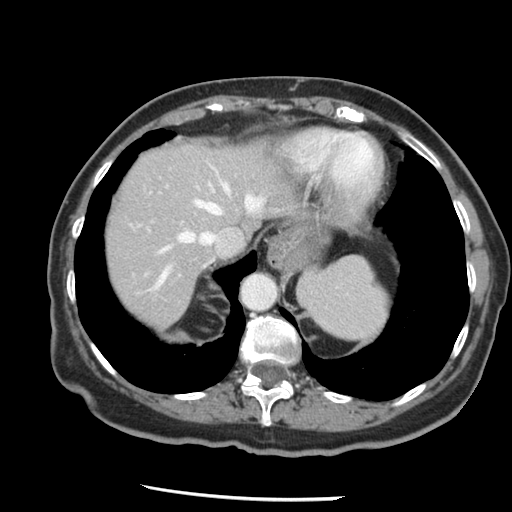
Contrast-enhanced abdominal CT, one axial slice. Position 111 of 148 along the scan axis. Reconstruction kernel STANDARD. 120 kVp. Intravenous contrast given. Soft-tissue window (W 400 / L 40 HU). 2.5 mm slice thickness. 512 × 512 image matrix. Female patient, age 85 years. Case-level facts recorded for this patient, not image findings: diagnosis: colorectal cancer liver metastases, imaged before liver resection.
Structures marked on this image (expert manual segmentation):
- hepatic veins: bounding box (x1, y1, x2, y2) in pixels: (156, 182, 262, 287)
- liver: (104, 141, 295, 328)
- planned liver remnant (the part of the liver to remain after resection): (104, 141, 295, 328)